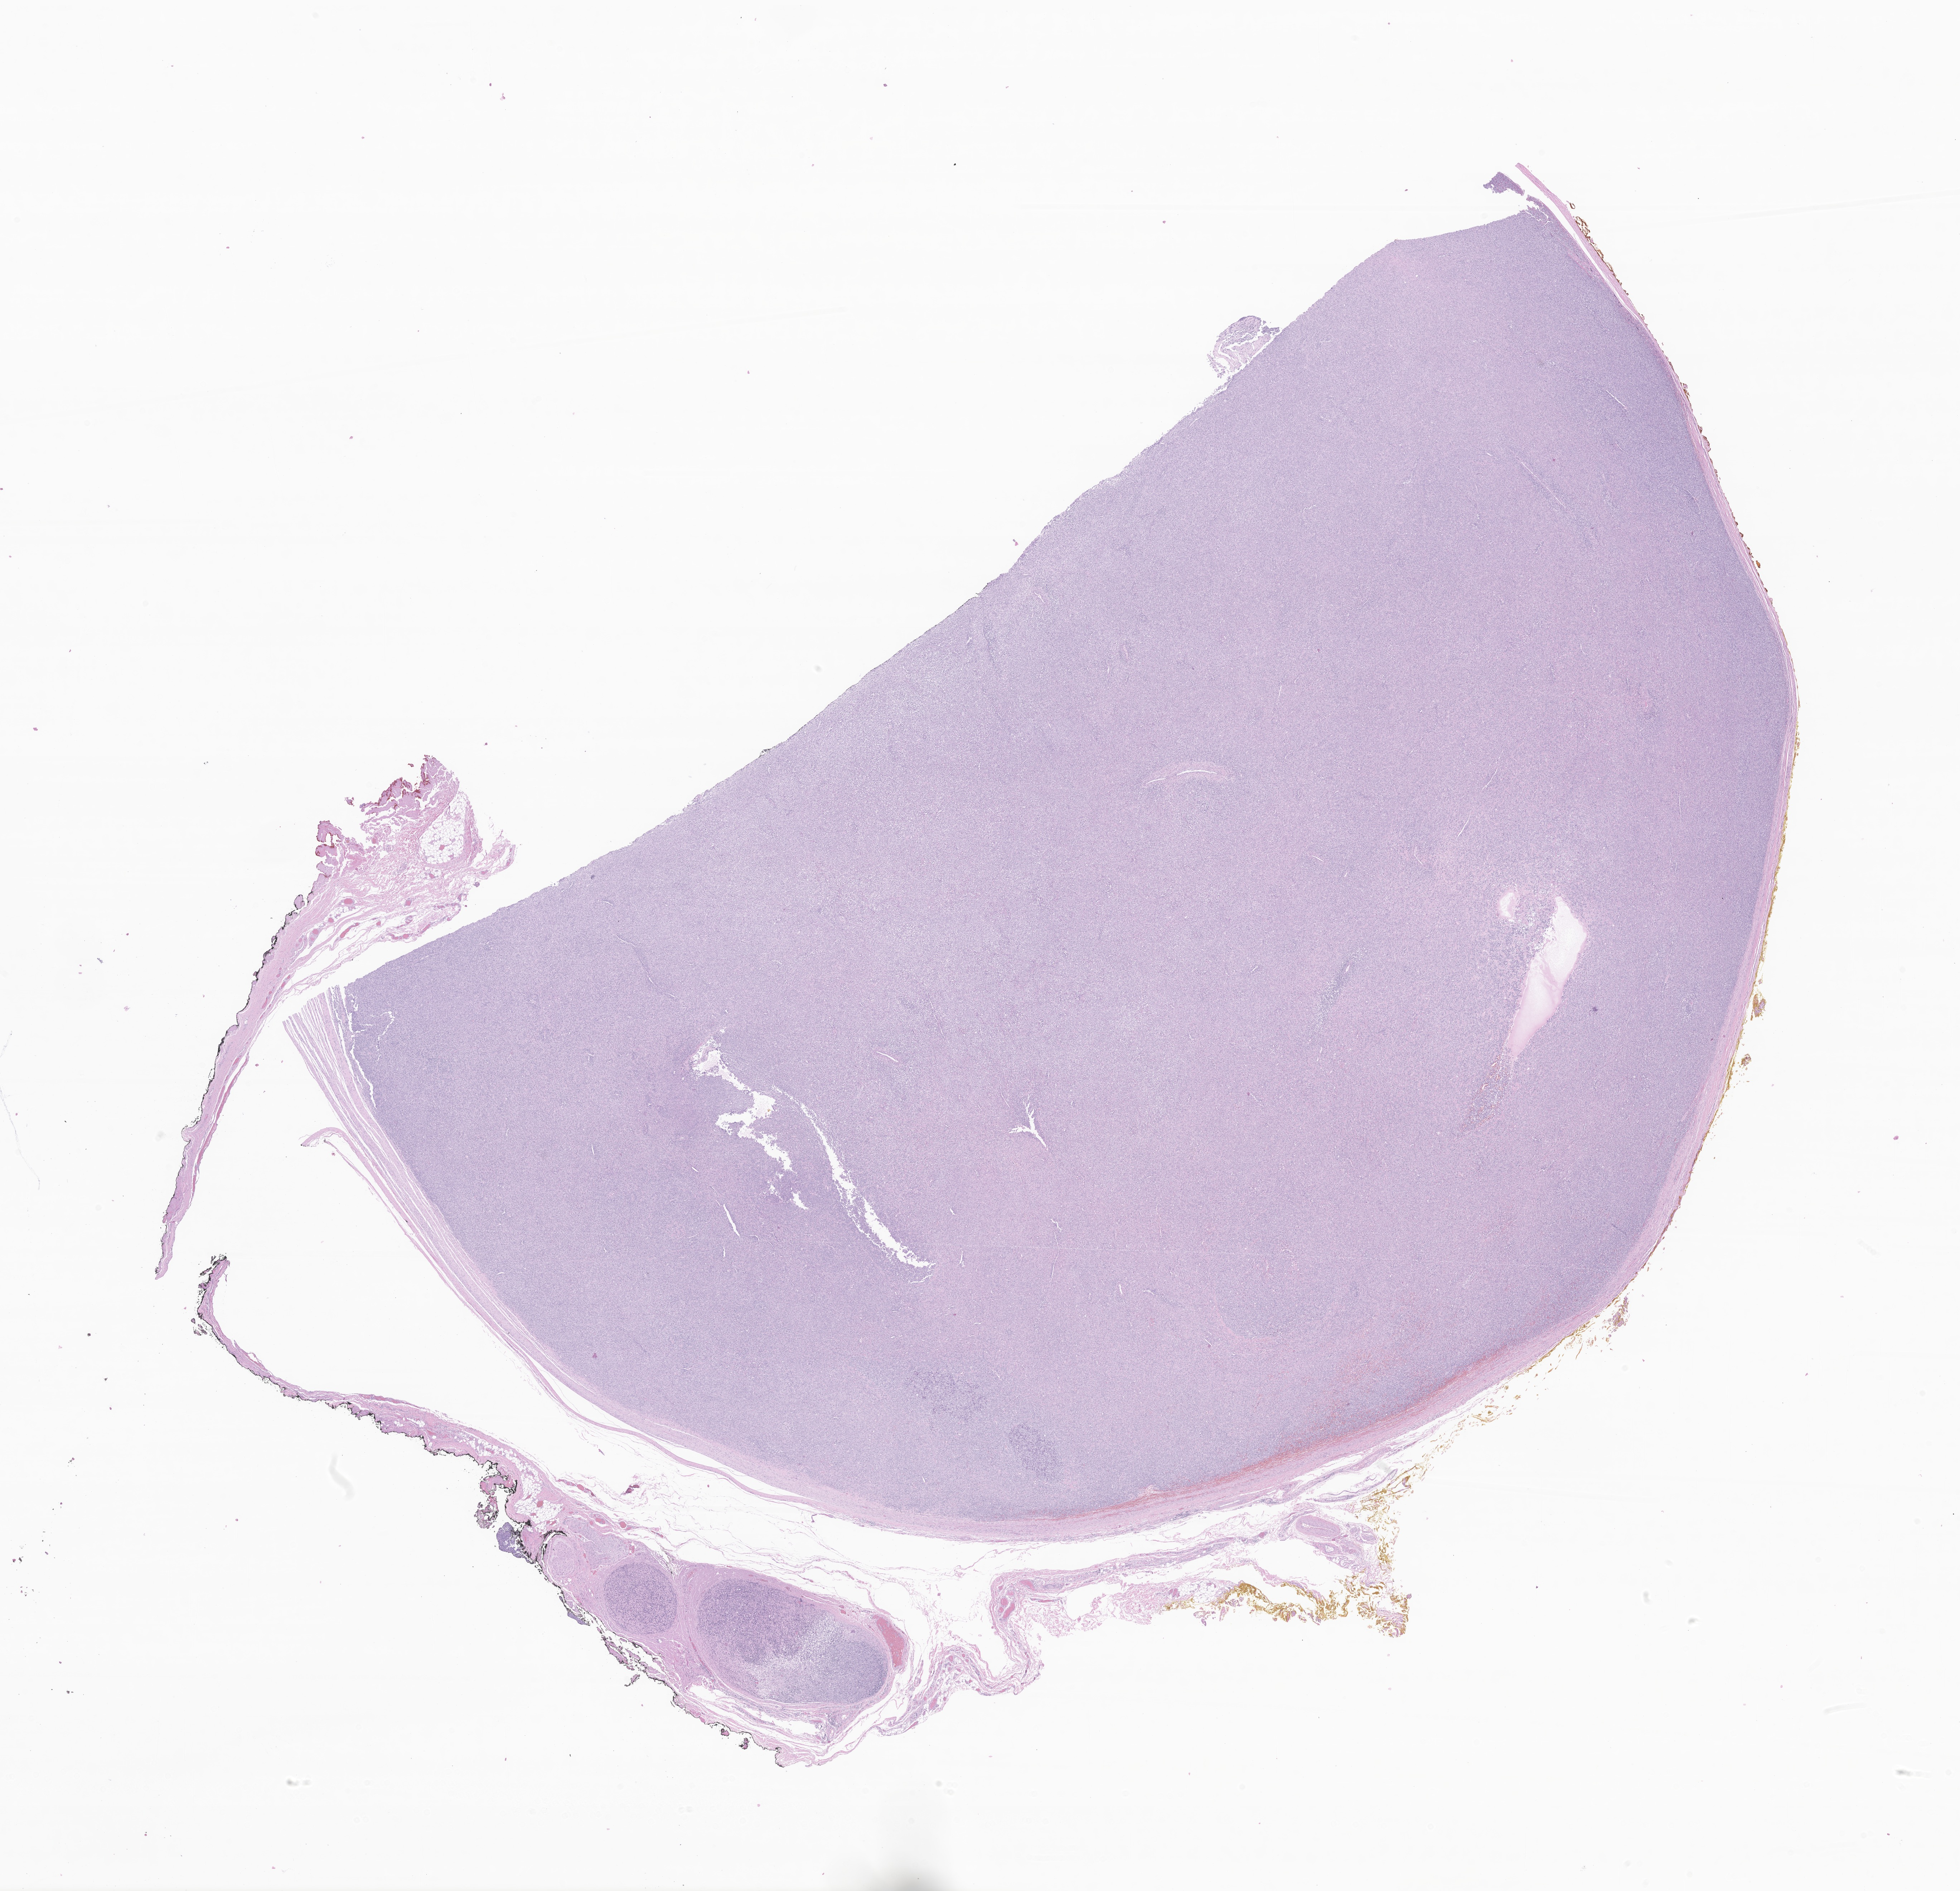
Haematoxylin and eosin whole-slide image of tumor tissue from the soft tissues of head and neck — whole scanned area (about 23.1 x 22.3 mm) shown as a low-resolution overview. Formalin-fixed paraffin-embedded section. Female patient, age 117 months (9 years 9 months).
Recorded diagnosis: Small cell sarcoma.